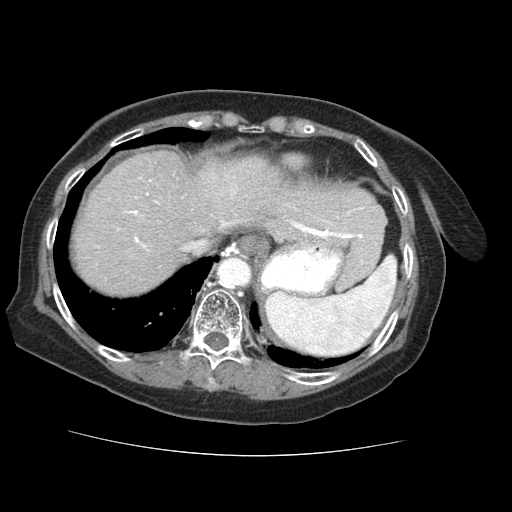
Contrast-enhanced abdominal CT (liver protocol), one axial slice. Slice 53 of 73 in the series (ordered by position). 120 kVp. Soft-tissue window (W 400 / L 40 HU). 2.5 mm slice thickness. 512 × 512 image matrix, field of view 360 × 360 mm. From the clinical record (not read from this slice): diagnosis: hepatocellular carcinoma (patient treated with transarterial chemoembolisation; whether this scan precedes or follows treatment is not stated here); TNM stage (as recorded): Stage-IVB; Child-Pugh class: A; tumour differentiation: well differentiated; tumour nodularity: uninodular.
Outlined on this slice (semi-automatic segmentation, software-assisted and operator-edited):
- abdominal aorta: box from (x=219, y=259) to (x=251, y=286) px
- liver parenchyma outside the tumour (the mass and vessels are separate outlines, so this box may not span the whole liver): (x=74, y=150)–(x=374, y=294)
- liver vessels: (x=118, y=178)–(x=363, y=248)